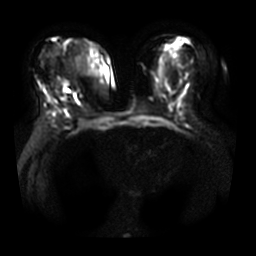
Breast MRI, one axial slice; position 13 of 33 along the scan axis; diffusion-weighted series; image 2 of 4 stored at this slice position (different b-values; order by instance number); 3 T; 256 × 256 image matrix, field of view 360 × 360 mm. Female patient.
Outlined on this slice (expert manual segmentation):
- tumour on diffusion-weighted imaging: bounding box (x1, y1, x2, y2) in pixels: (62, 80, 67, 85)